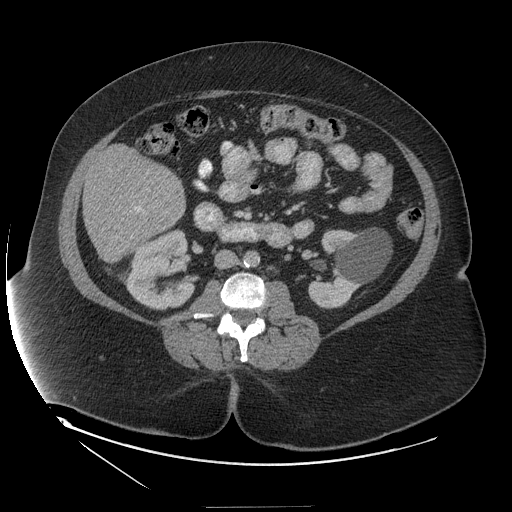
Contrast-enhanced abdominal CT (liver protocol), one axial slice; position 42 of 127 along the scan axis; 140 kVp; soft-tissue window (W 400 / L 40 HU); 2.5 mm slice thickness; 512 × 512 image matrix, field of view 480 × 480 mm. From the clinical record (not read from this slice): diagnosis: hepatocellular carcinoma (patient treated with transarterial chemoembolisation; whether this scan precedes or follows treatment is not stated here); TNM stage (as recorded): Stage-II; Child-Pugh class: A; tumour differentiation: well differentiated; tumour nodularity: multinodular.
Outlined on this slice (semi-automatic segmentation, software-assisted and operator-edited):
- liver parenchyma outside the tumour (the mass and vessels are separate outlines, so this box may not span the whole liver): bounding box [x1, y1, x2, y2] px = [82, 144, 186, 262]
- liver vessels: [135, 207, 141, 211]